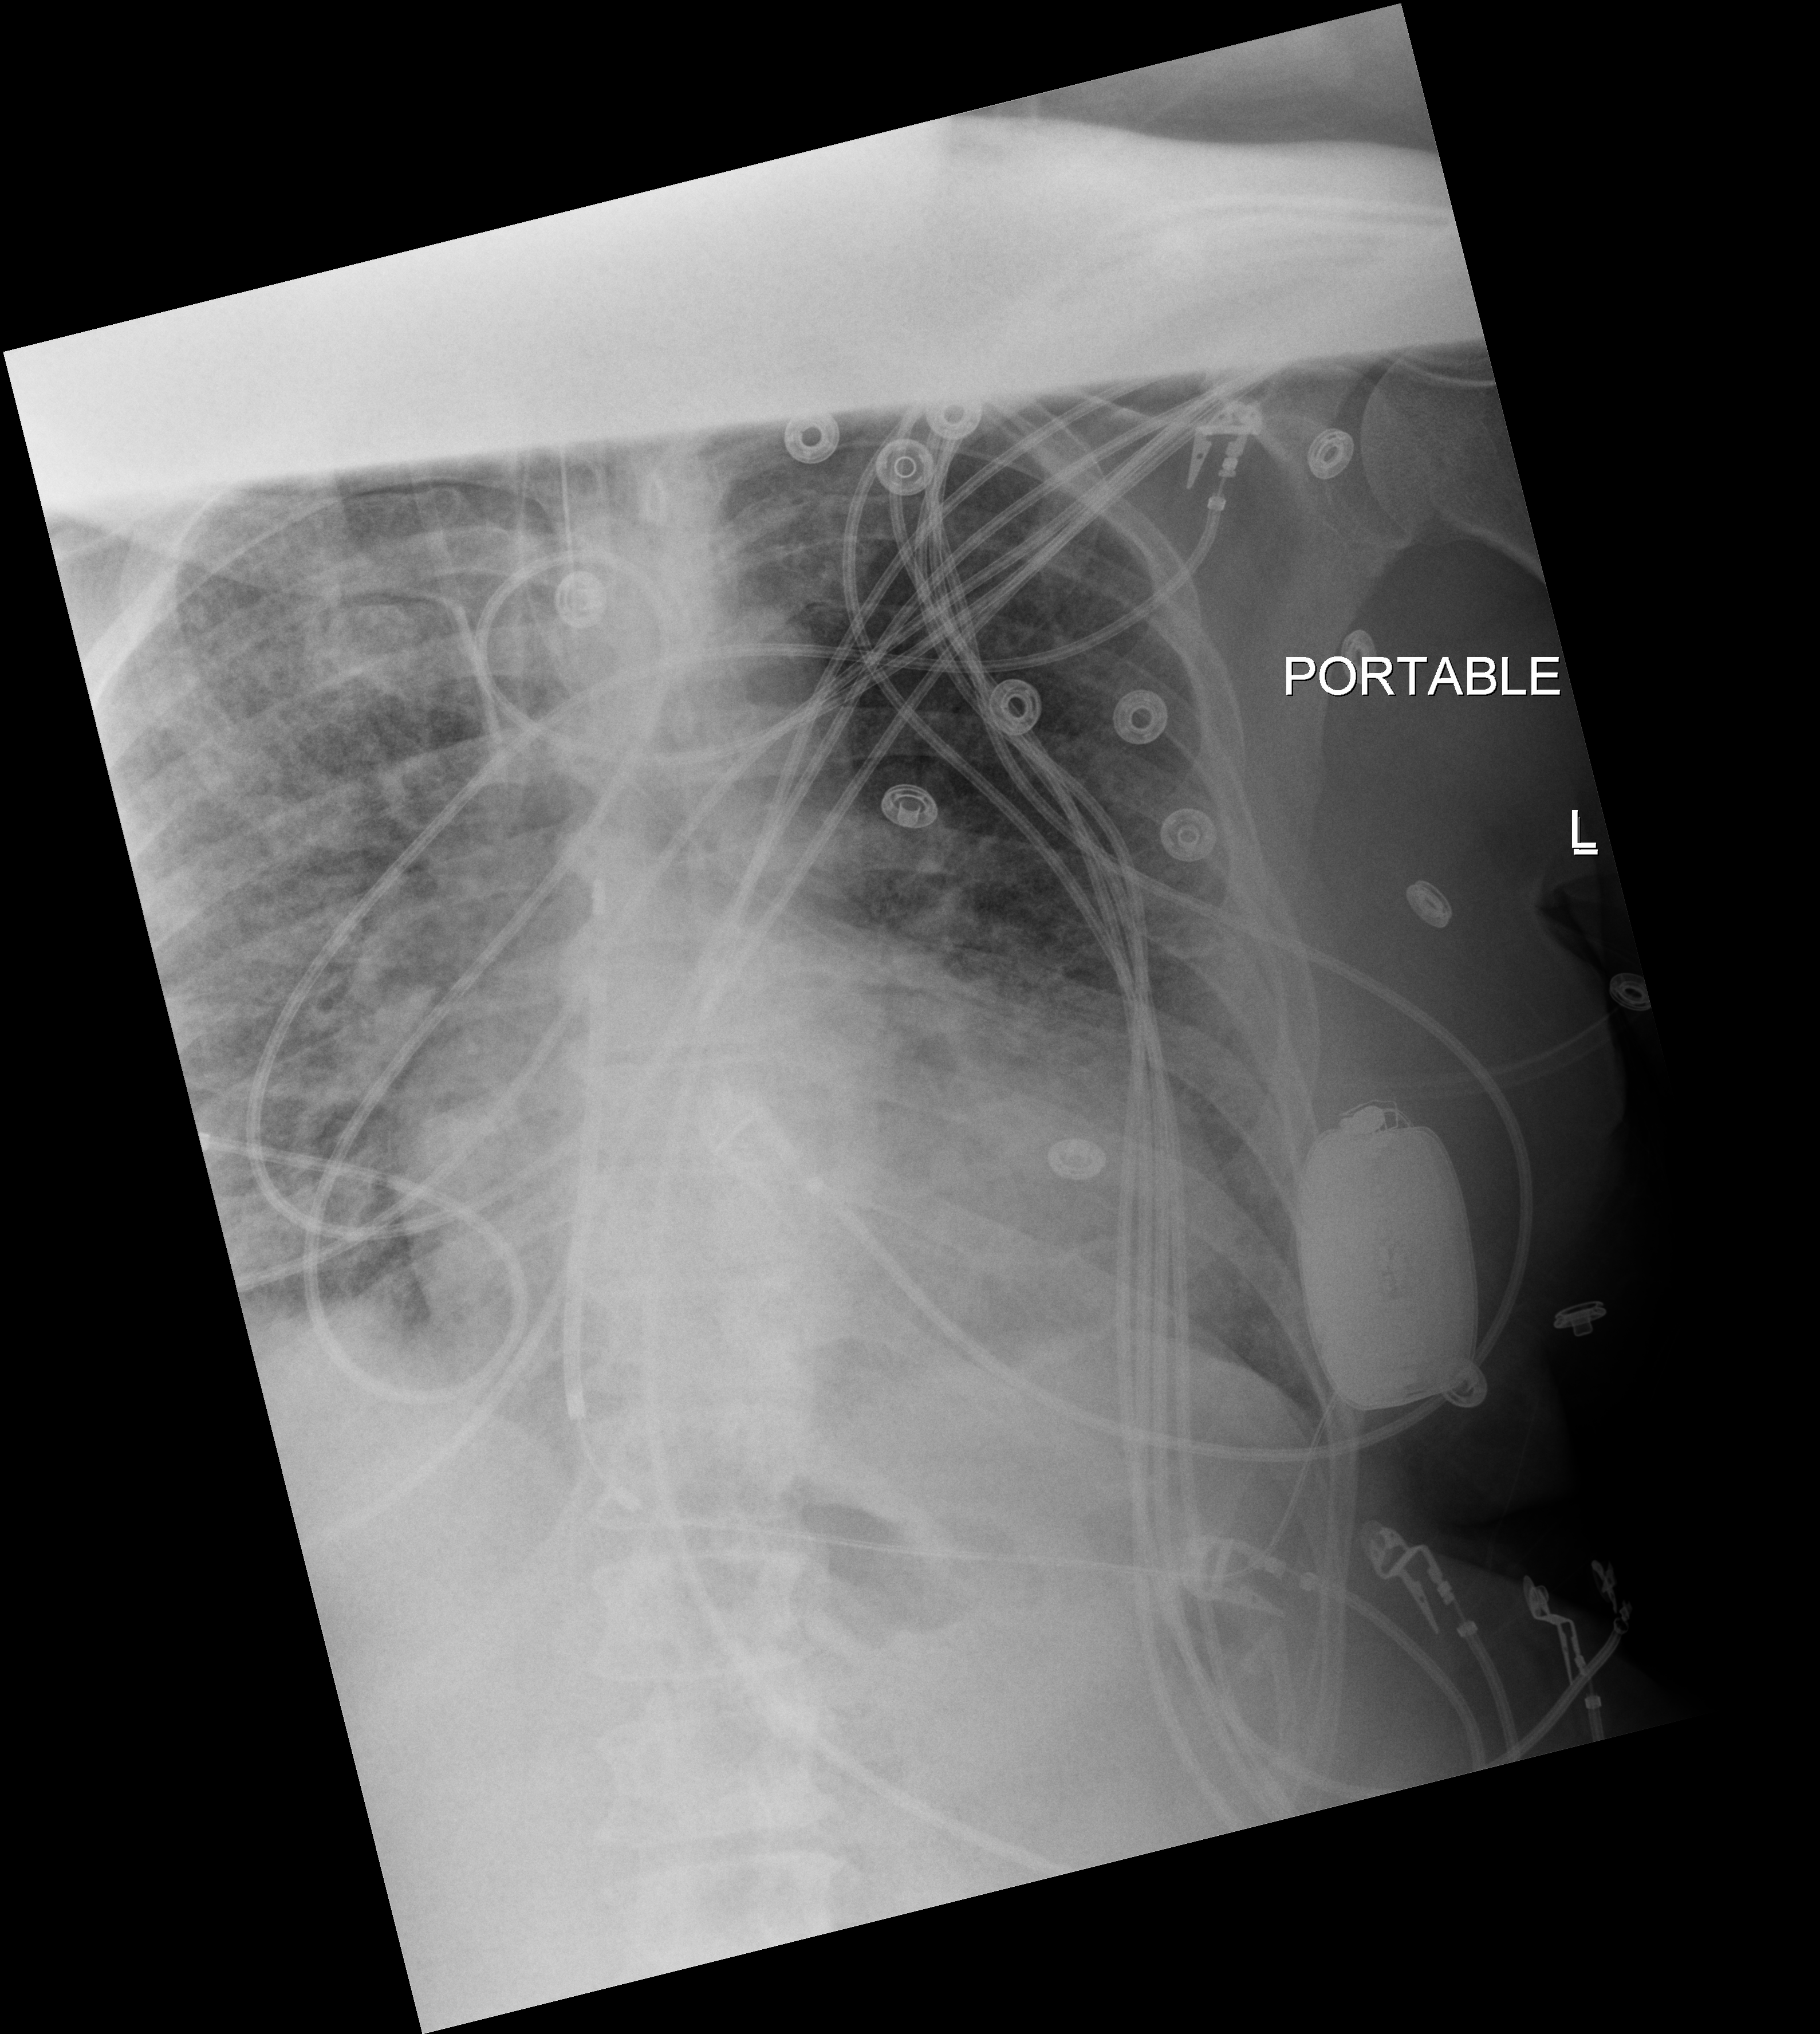
Portable chest radiograph, anteroposterior (AP) projection. Male patient hospitalised with COVID-19, age 60–74 years.
Hospital-stay facts (about this admission, not read from this image; timing relative to this image not recorded): chronic kidney disease (admission record): no; admitted to intensive care during this hospital stay: yes; smoking status (admission record): never.